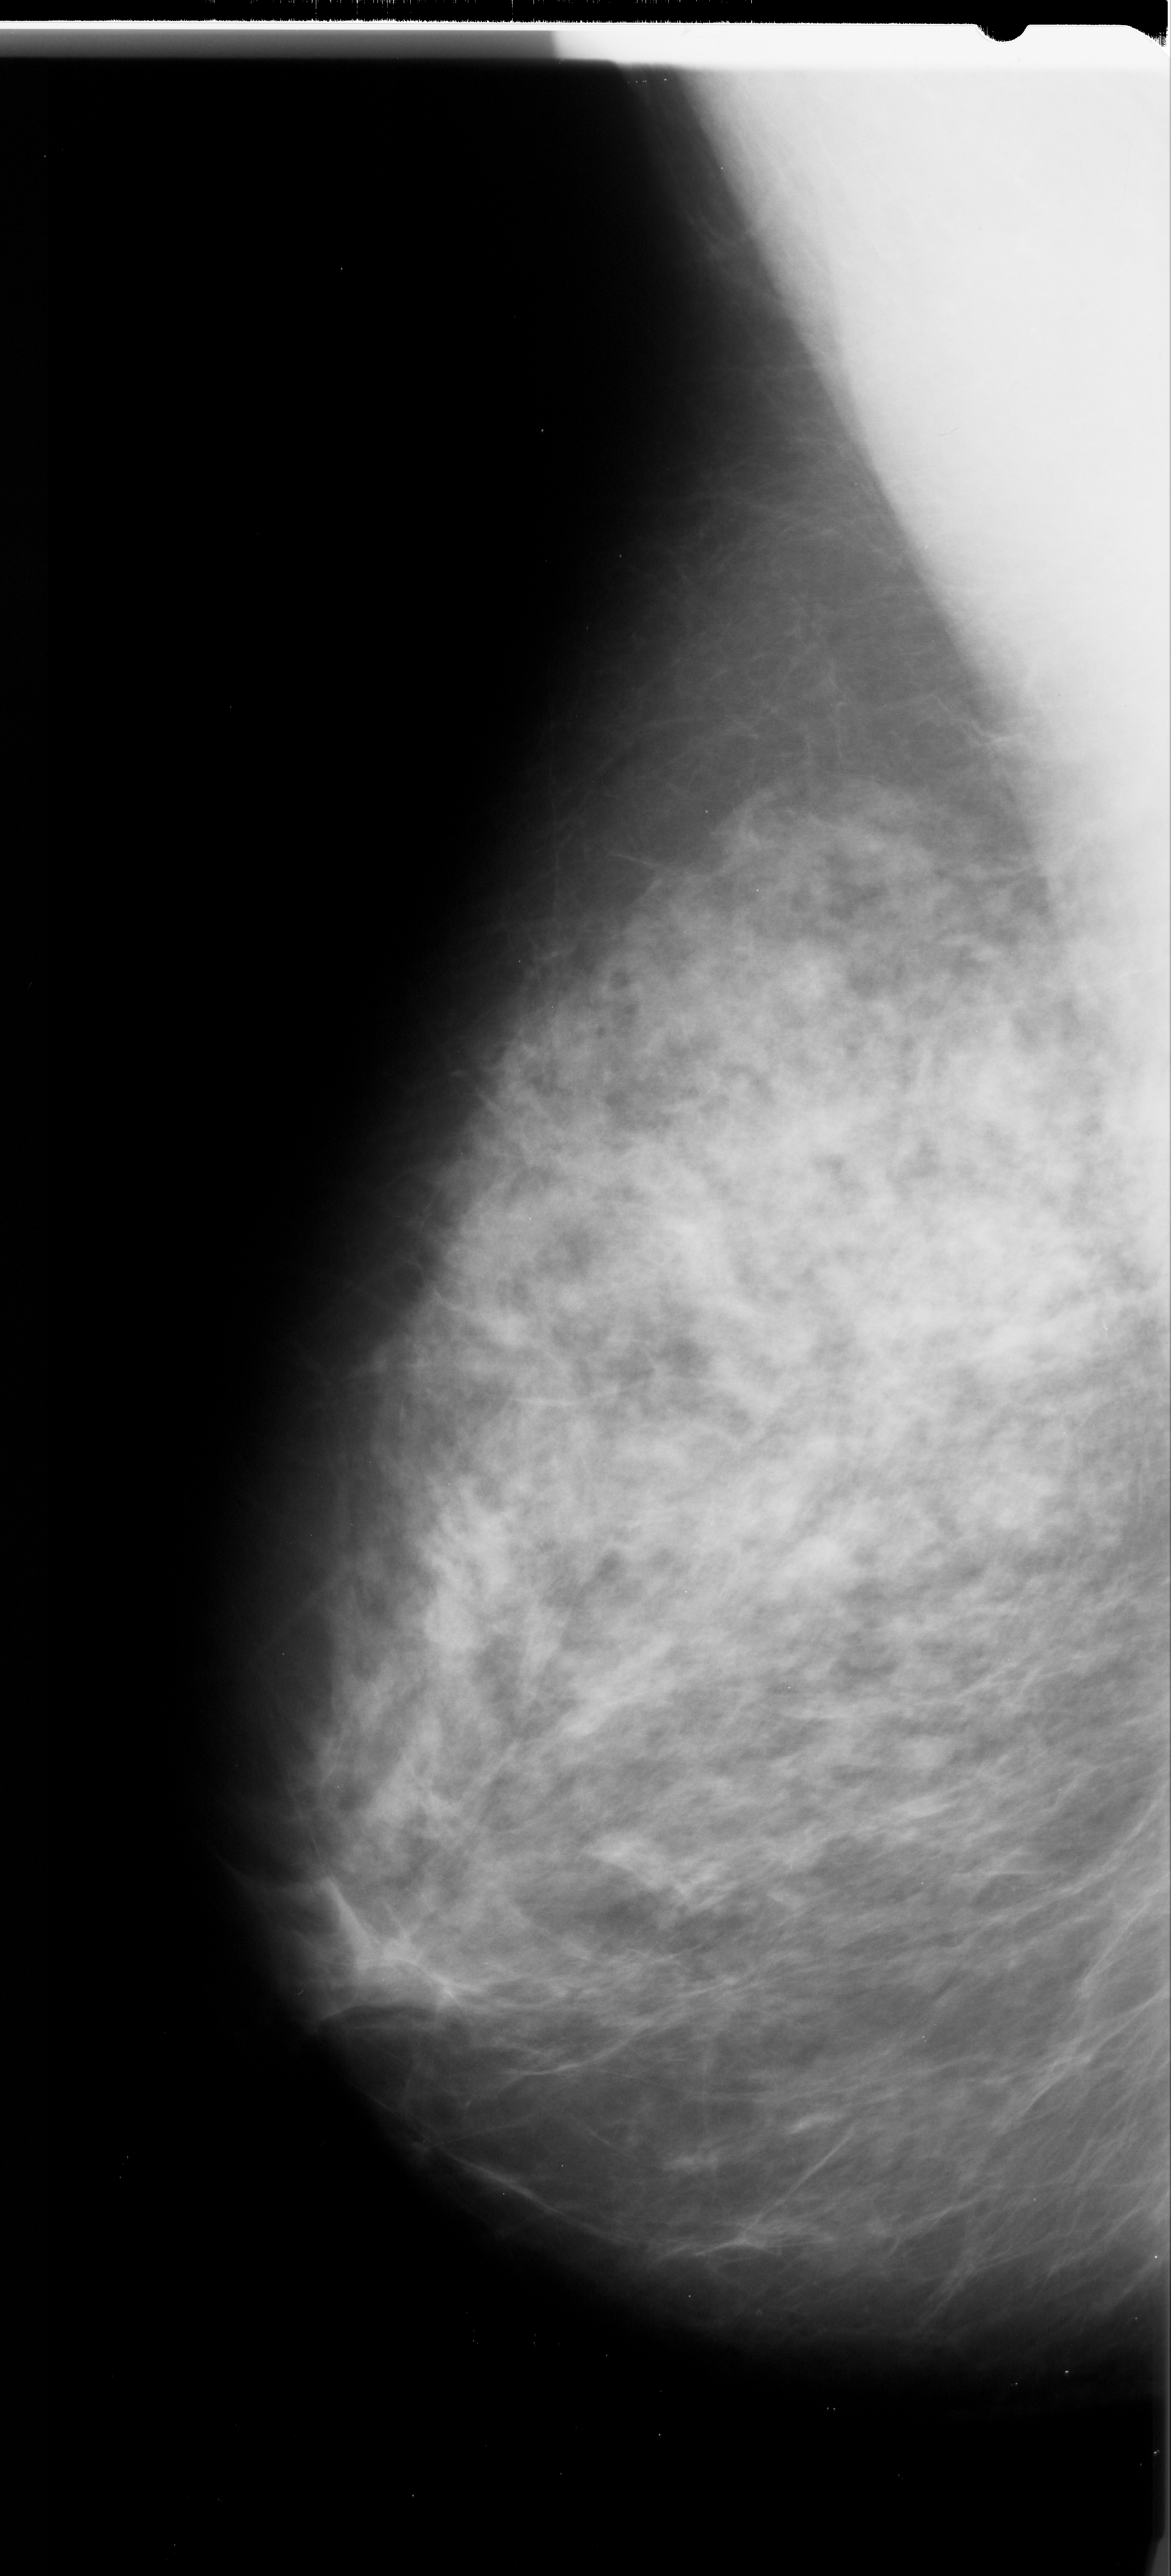
Mammogram (digitized film). Left breast. Mediolateral oblique (MLO) view. Breast composition: heterogeneously dense (BI-RADS density category 3 of 4). 1171 × 2576 image matrix.
Expert-marked regions of interest on this film, with their recorded descriptors:
- calcifications, morphology pleomorphic, distribution clustered; BI-RADS assessment category 4; pathology result (as recorded, not read from the image): malignant: box from (x=672, y=1411) to (x=768, y=1577) px